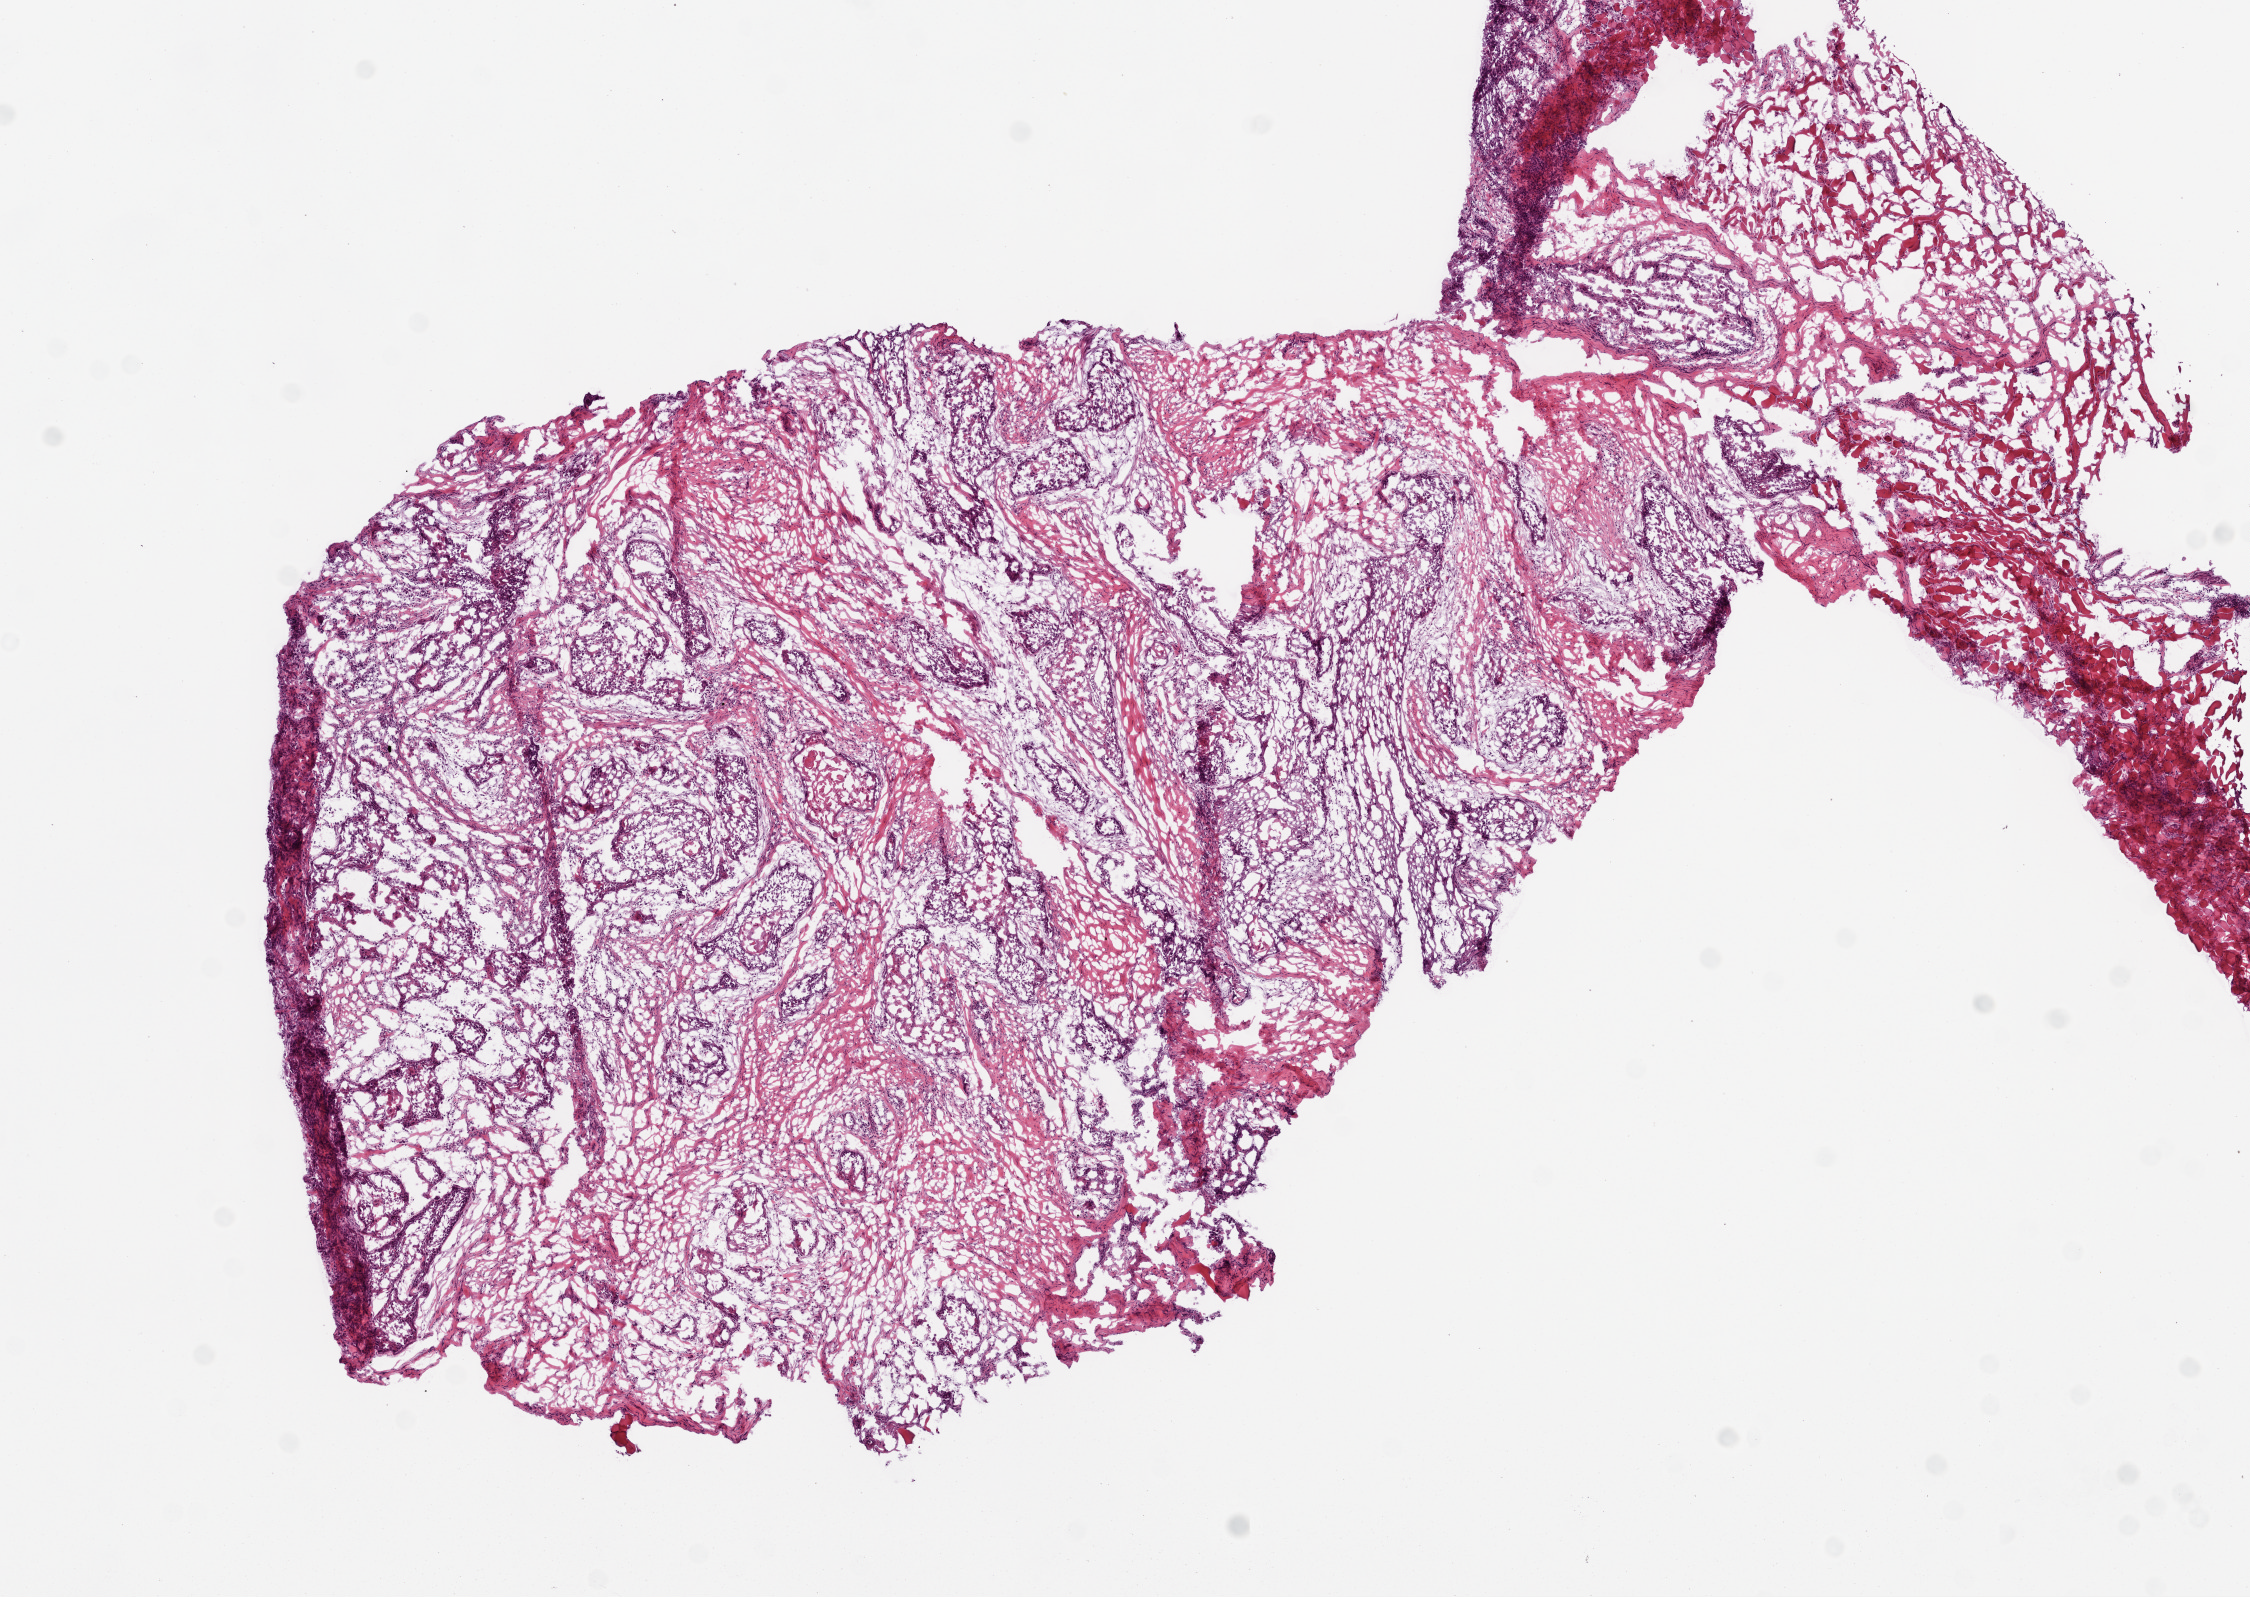
Whole-slide histology image, Hematoxylin and eosin (H&E) stained, low-resolution overview of the scanned area, about 9.0 x 6.4 mm (acquisition: 20x scan), frozen section from the bottom of the tissue portion, sample: primary tumour, head and neck. Male, age 55 years at initial diagnosis. Histologic grade: G2 (moderately differentiated). Composition of this section per pathologist review: tumour cells 75%, tumour nuclei 80%, normal cells 10%, stromal cells 15%, necrosis 0%.
* AJCC pathologic stage: IVA
* diagnosis: Squamous cell carcinoma, NOS (floor of mouth, NOS)
* TNM: T4a N2c M0